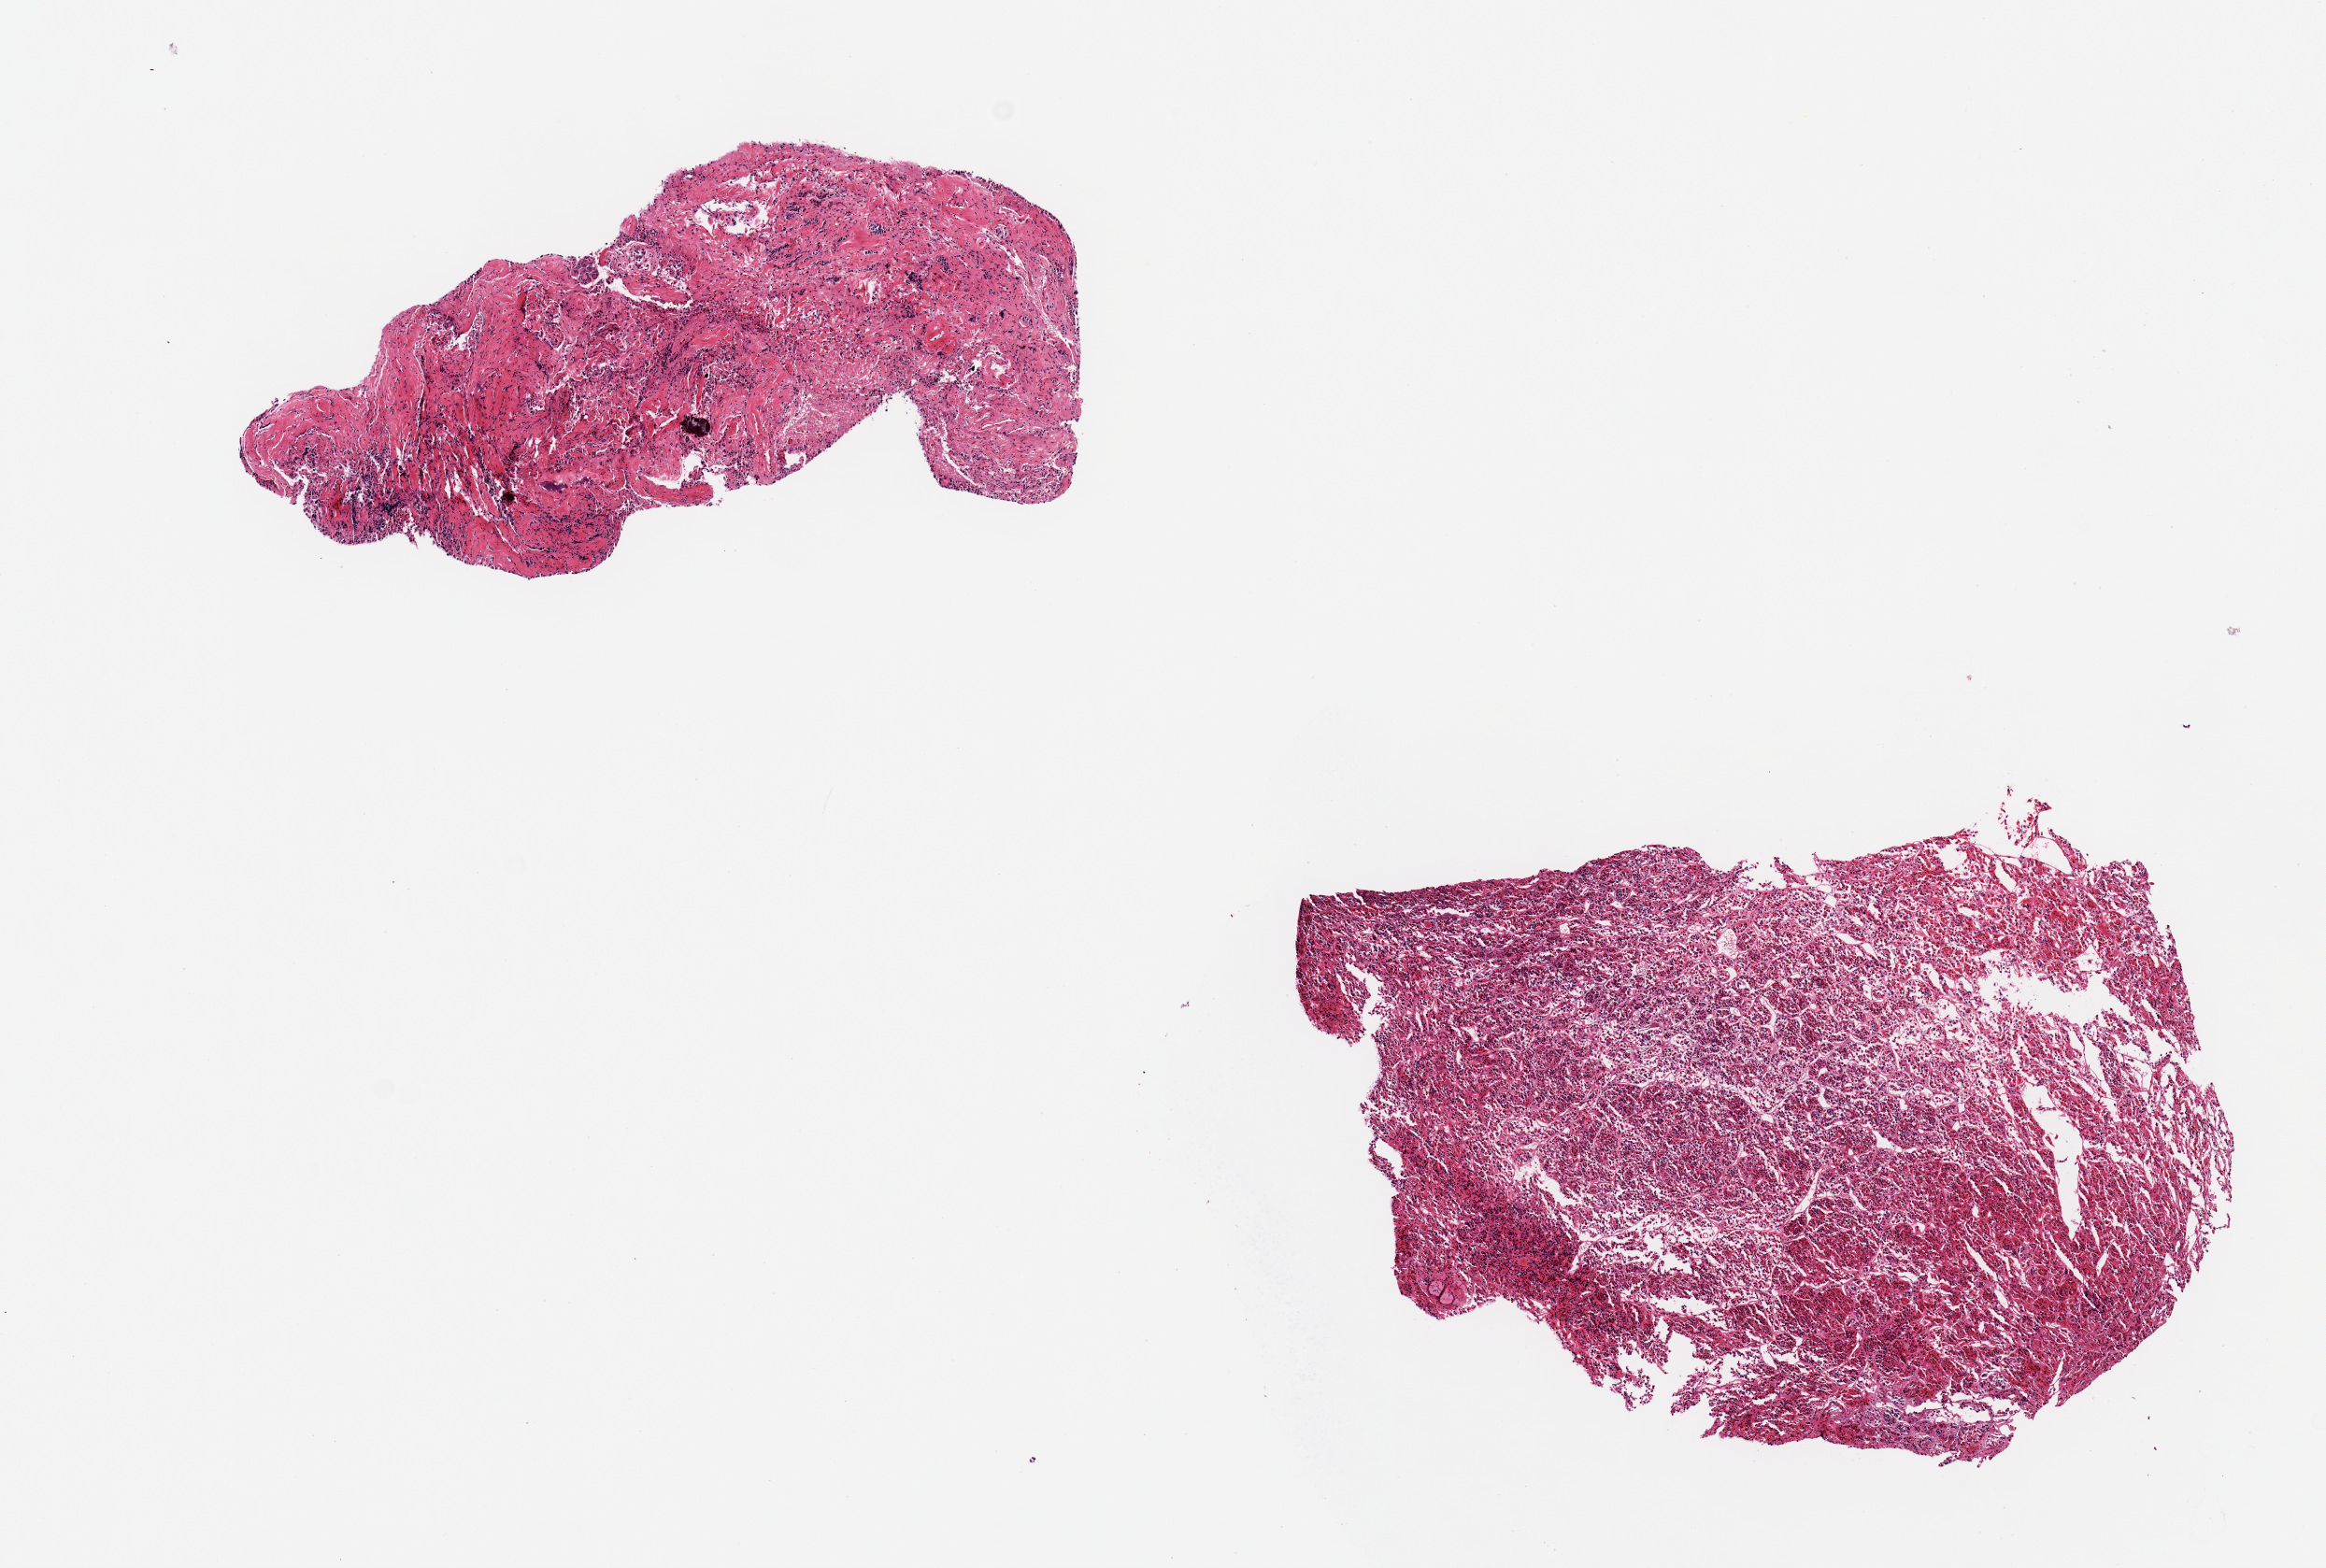
Digitized hematoxylin and eosin (H&E)-stained section, whole scanned area (about 9.8 x 6.6 mm, from a 20x scan) shown as a low-resolution overview, PAXgene-fixed paraffin-embedded (PFPE) section, target tissue: cerebellum, donor tissue sample.
• pathologist's review note for this sample: 2 pieces of pituitary; smaller piece is mostly fibrous tissue